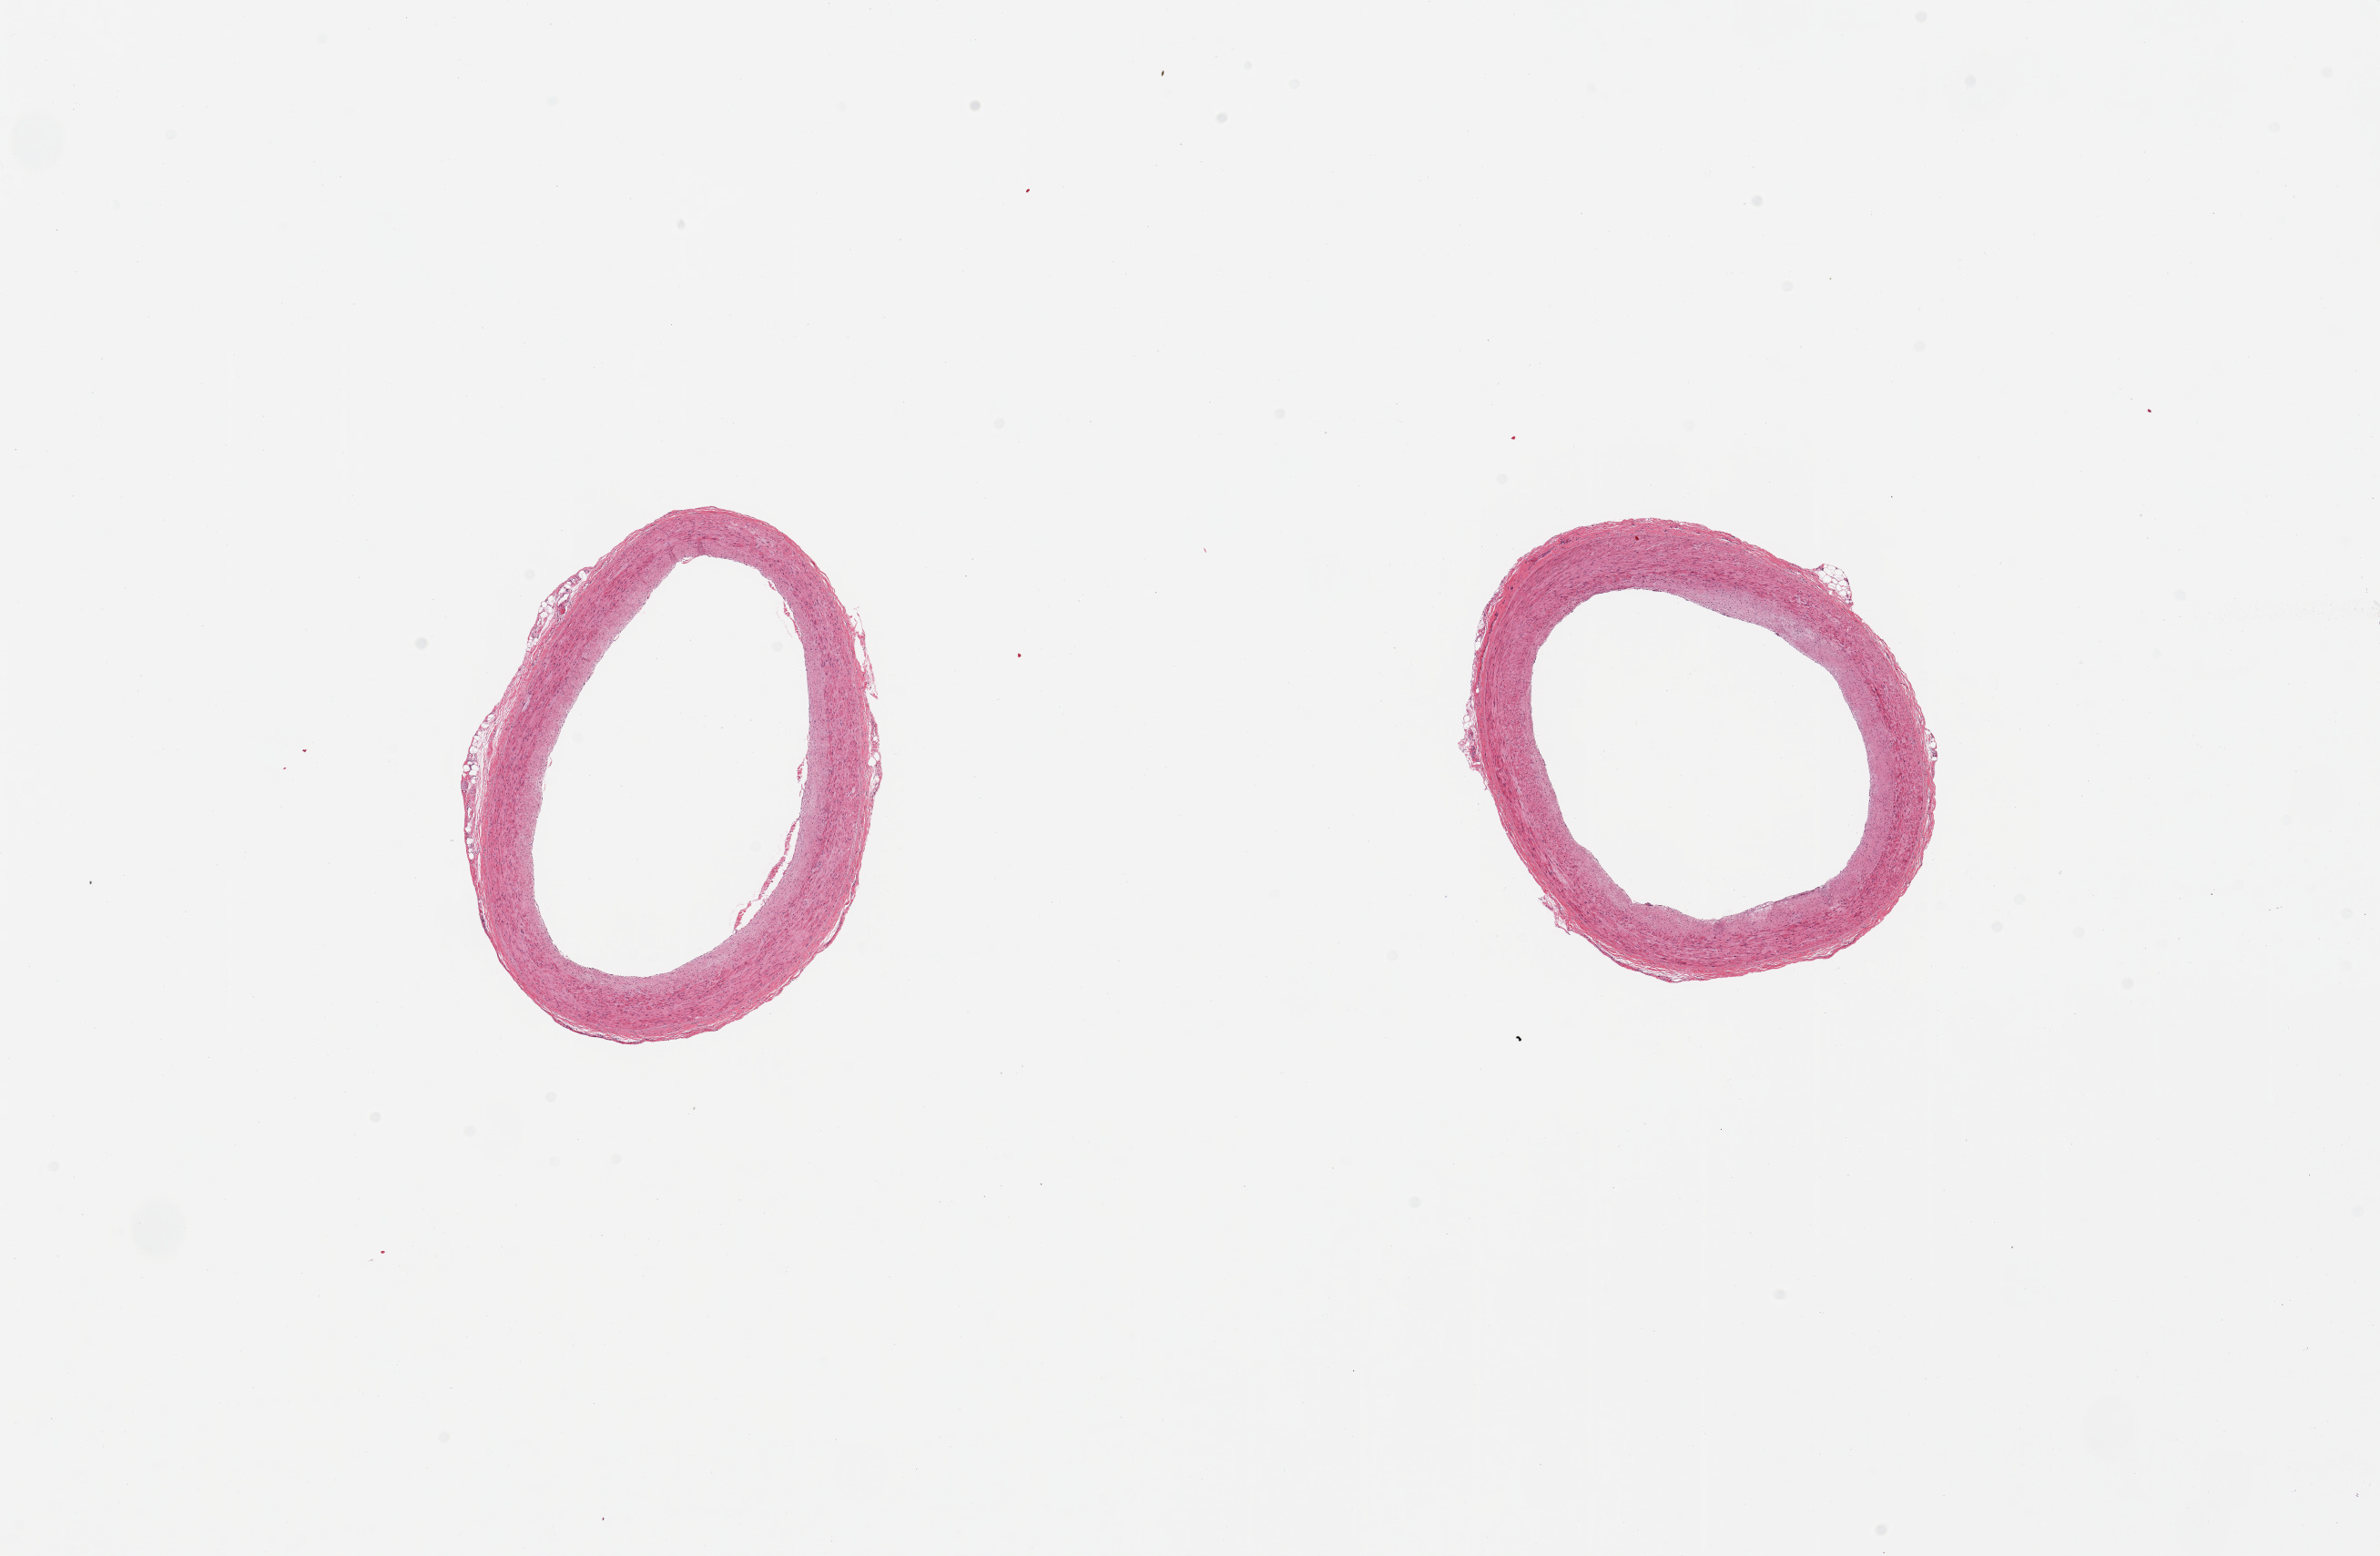
Digitized hematoxylin and eosin (H&E)-stained section — whole scanned area (about 20.7 x 13.5 mm, acquisition: 20x scan) shown as a low-resolution overview, PAXgene-fixed, paraffin-embedded tissue, target tissue: coronary artery, donor tissue sample. Male donor.
- pathologist's review note for this sample: 2 pieces, minimal atherosis